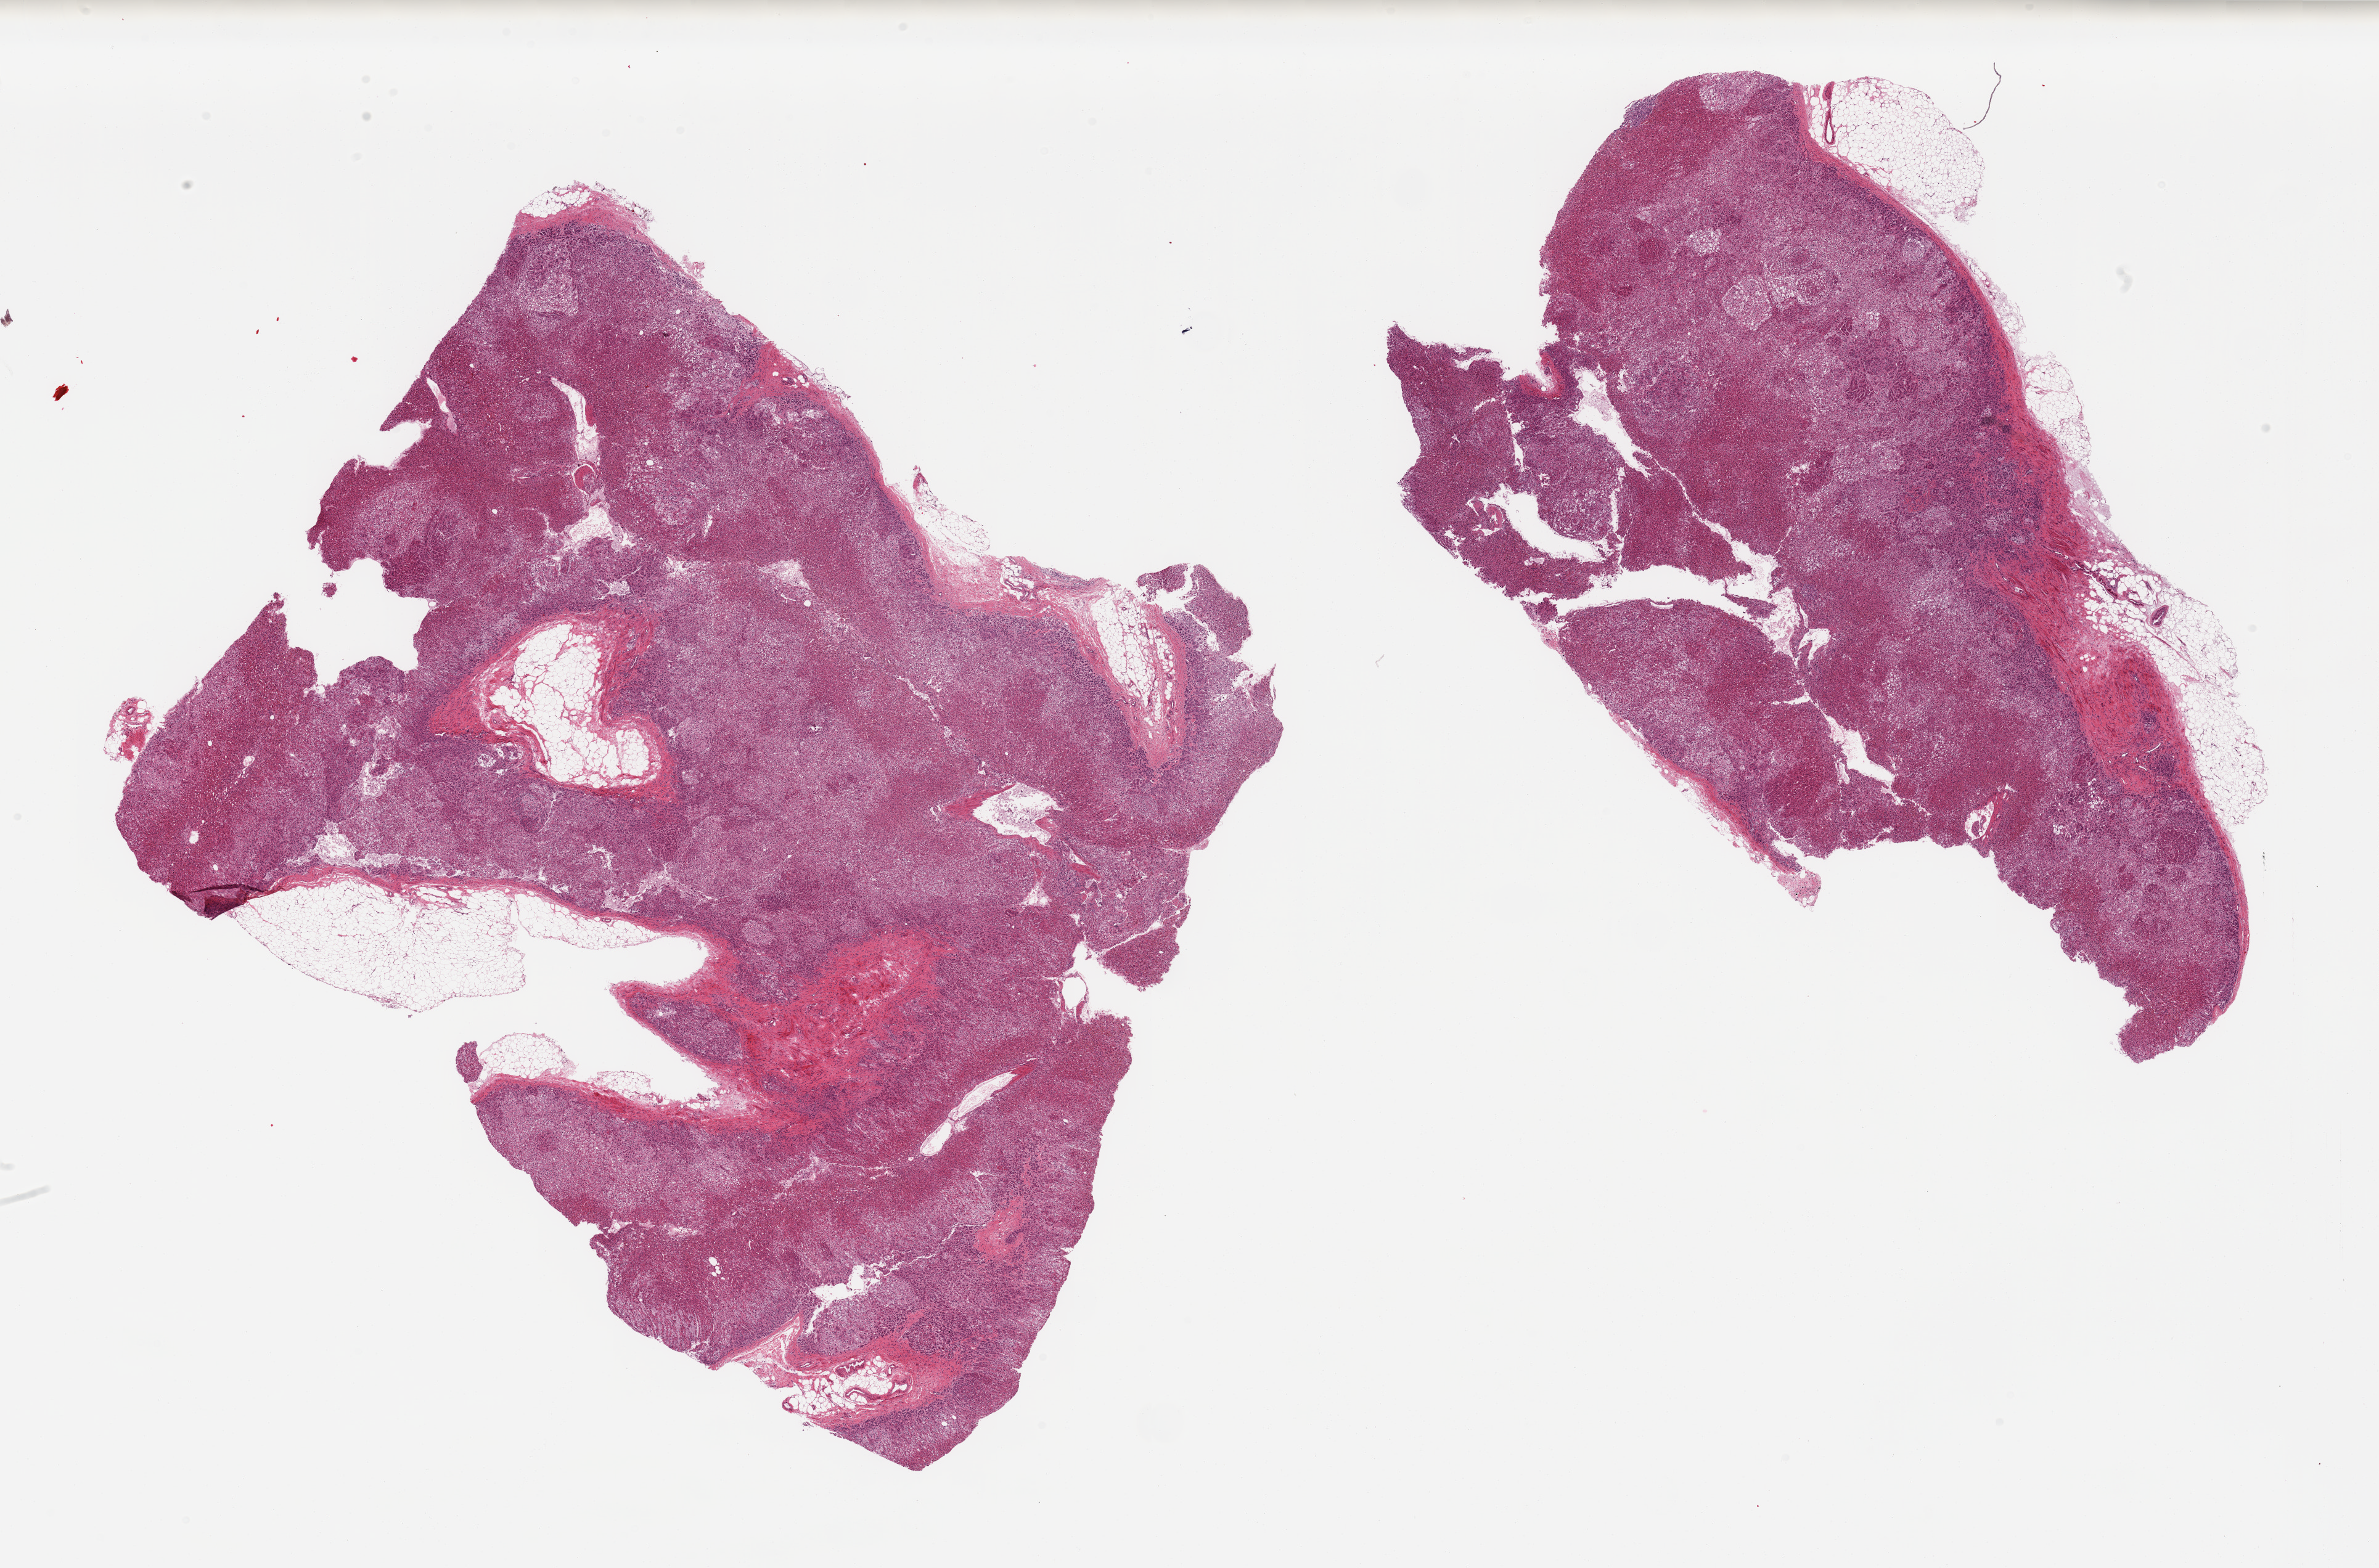
Whole-slide image, H&E stain, shown as a low-resolution overview of the whole scanned area (about 30.5 x 20.1 mm, acquisition: 20x scan); PAXgene-fixed paraffin-embedded (PFPE) section; target tissue: adrenal gland; tissue donor sample. Male donor.
Pathologist's review note for this sample: 2 pieces; cortex; 10% internal and external fat.